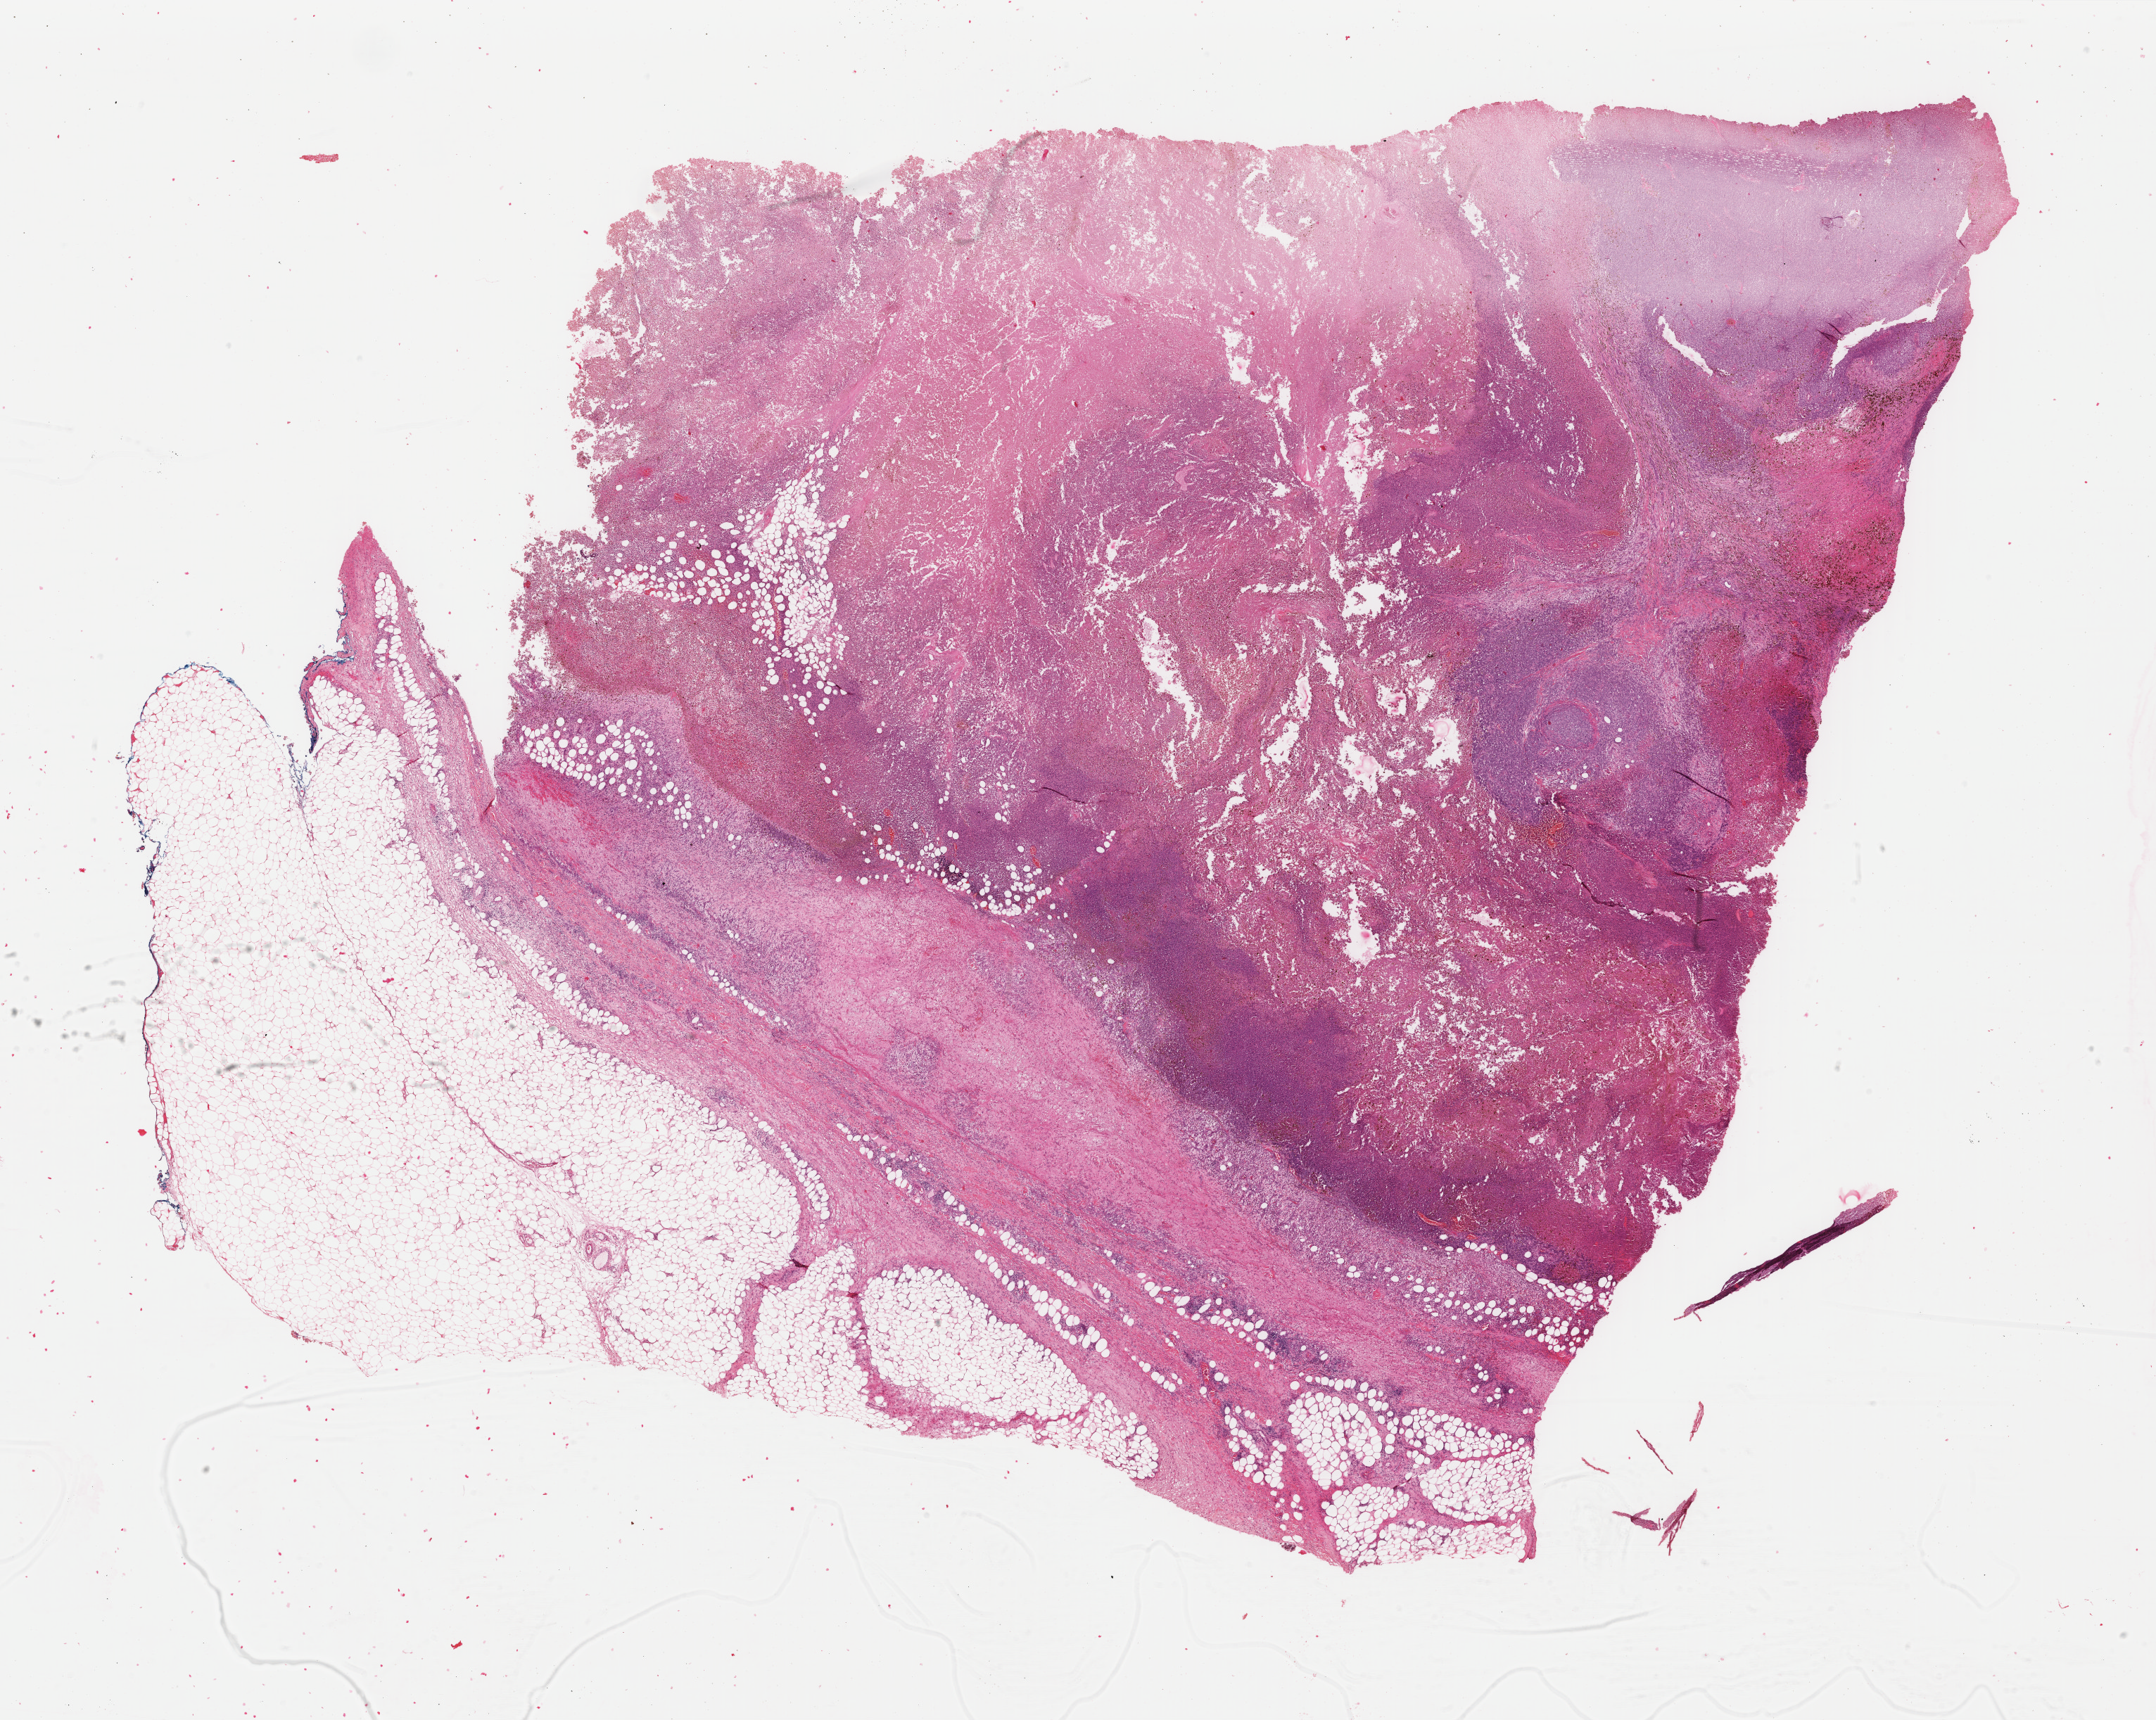
Digitized H&E-stained tissue section (whole slide), low-resolution overview of the scanned area, about 24.3 x 19.4 mm, FFPE section, skin, primary tumour sample. Patient: male, age at initial diagnosis 57 years.
Pathologic diagnosis: Malignant melanoma, NOS.